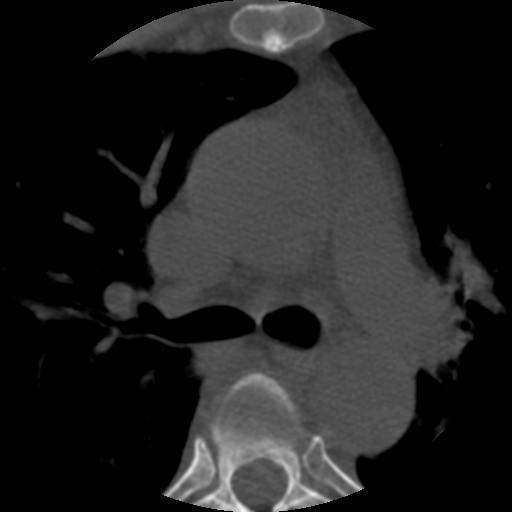
CT including the spine, one axial slice. Position 382 of 508 along the scan axis. Reconstruction kernel STANDARD. 120 kVp. Bone window (W 1800 / L 400 HU). 1.25 mm slice thickness. 512 × 512 image matrix. Patient age 57 years. From the clinical record (not read from this slice): primary cancer: prostate.
Annotated regions visible in this slice (semi-automatic segmentation, software-assisted and operator-edited):
- T4 vertebra: bounding box [x1, y1, x2, y2] px = [224, 377, 305, 437]
- T5 vertebra: [196, 374, 327, 512]